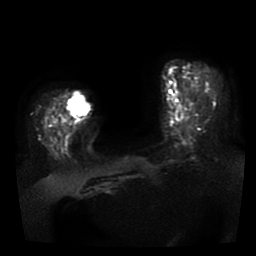
Breast MRI, one axial slice; slice 13 of 41 in the series (ordered by position); diffusion-weighted series; image 2 of 4 stored at this slice position (different b-values; order by instance number); 1.5 T; 5 mm slice thickness; 256 × 256 image matrix, field of view 330 × 330 mm. Female patient.
Structures marked on this image (manually delineated by an expert):
- tumour on diffusion-weighted imaging: box from (x=66, y=94) to (x=89, y=118) px